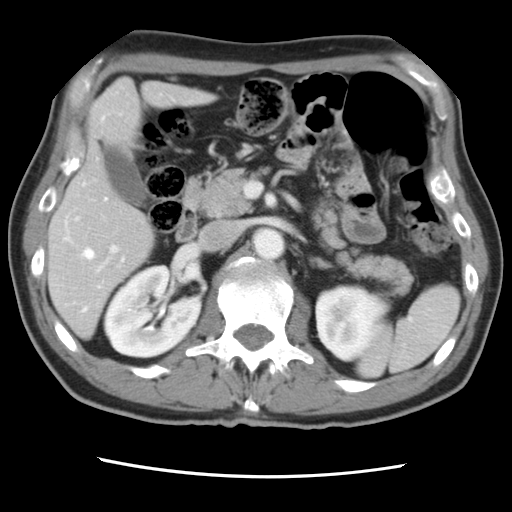
Contrast-enhanced abdominal CT, one axial slice; slice 41 of 83 in the series (ordered by position); 120 kVp; intravenous contrast given; soft-tissue window (W 400 / L 40 HU); 5 mm slice thickness; 512 × 512 image matrix, field of view 321 × 321 mm. Male patient, age 69 years. Case-level facts recorded for this patient, not image findings: diagnosis: colorectal cancer liver metastases, imaged before liver resection; multiple liver metastases: yes; largest metastasis: 3.5 cm; chemotherapy before resection: yes.
Outlined on this slice (expert manual segmentation):
- hepatic veins: bounding box <66,118,124,311> (left, top, right, bottom; pixels)
- liver: <50,80,208,336>
- planned liver remnant (the part of the liver to remain after resection): <50,149,154,337>
- portal vein (with intrahepatic branches): <74,182,119,273>